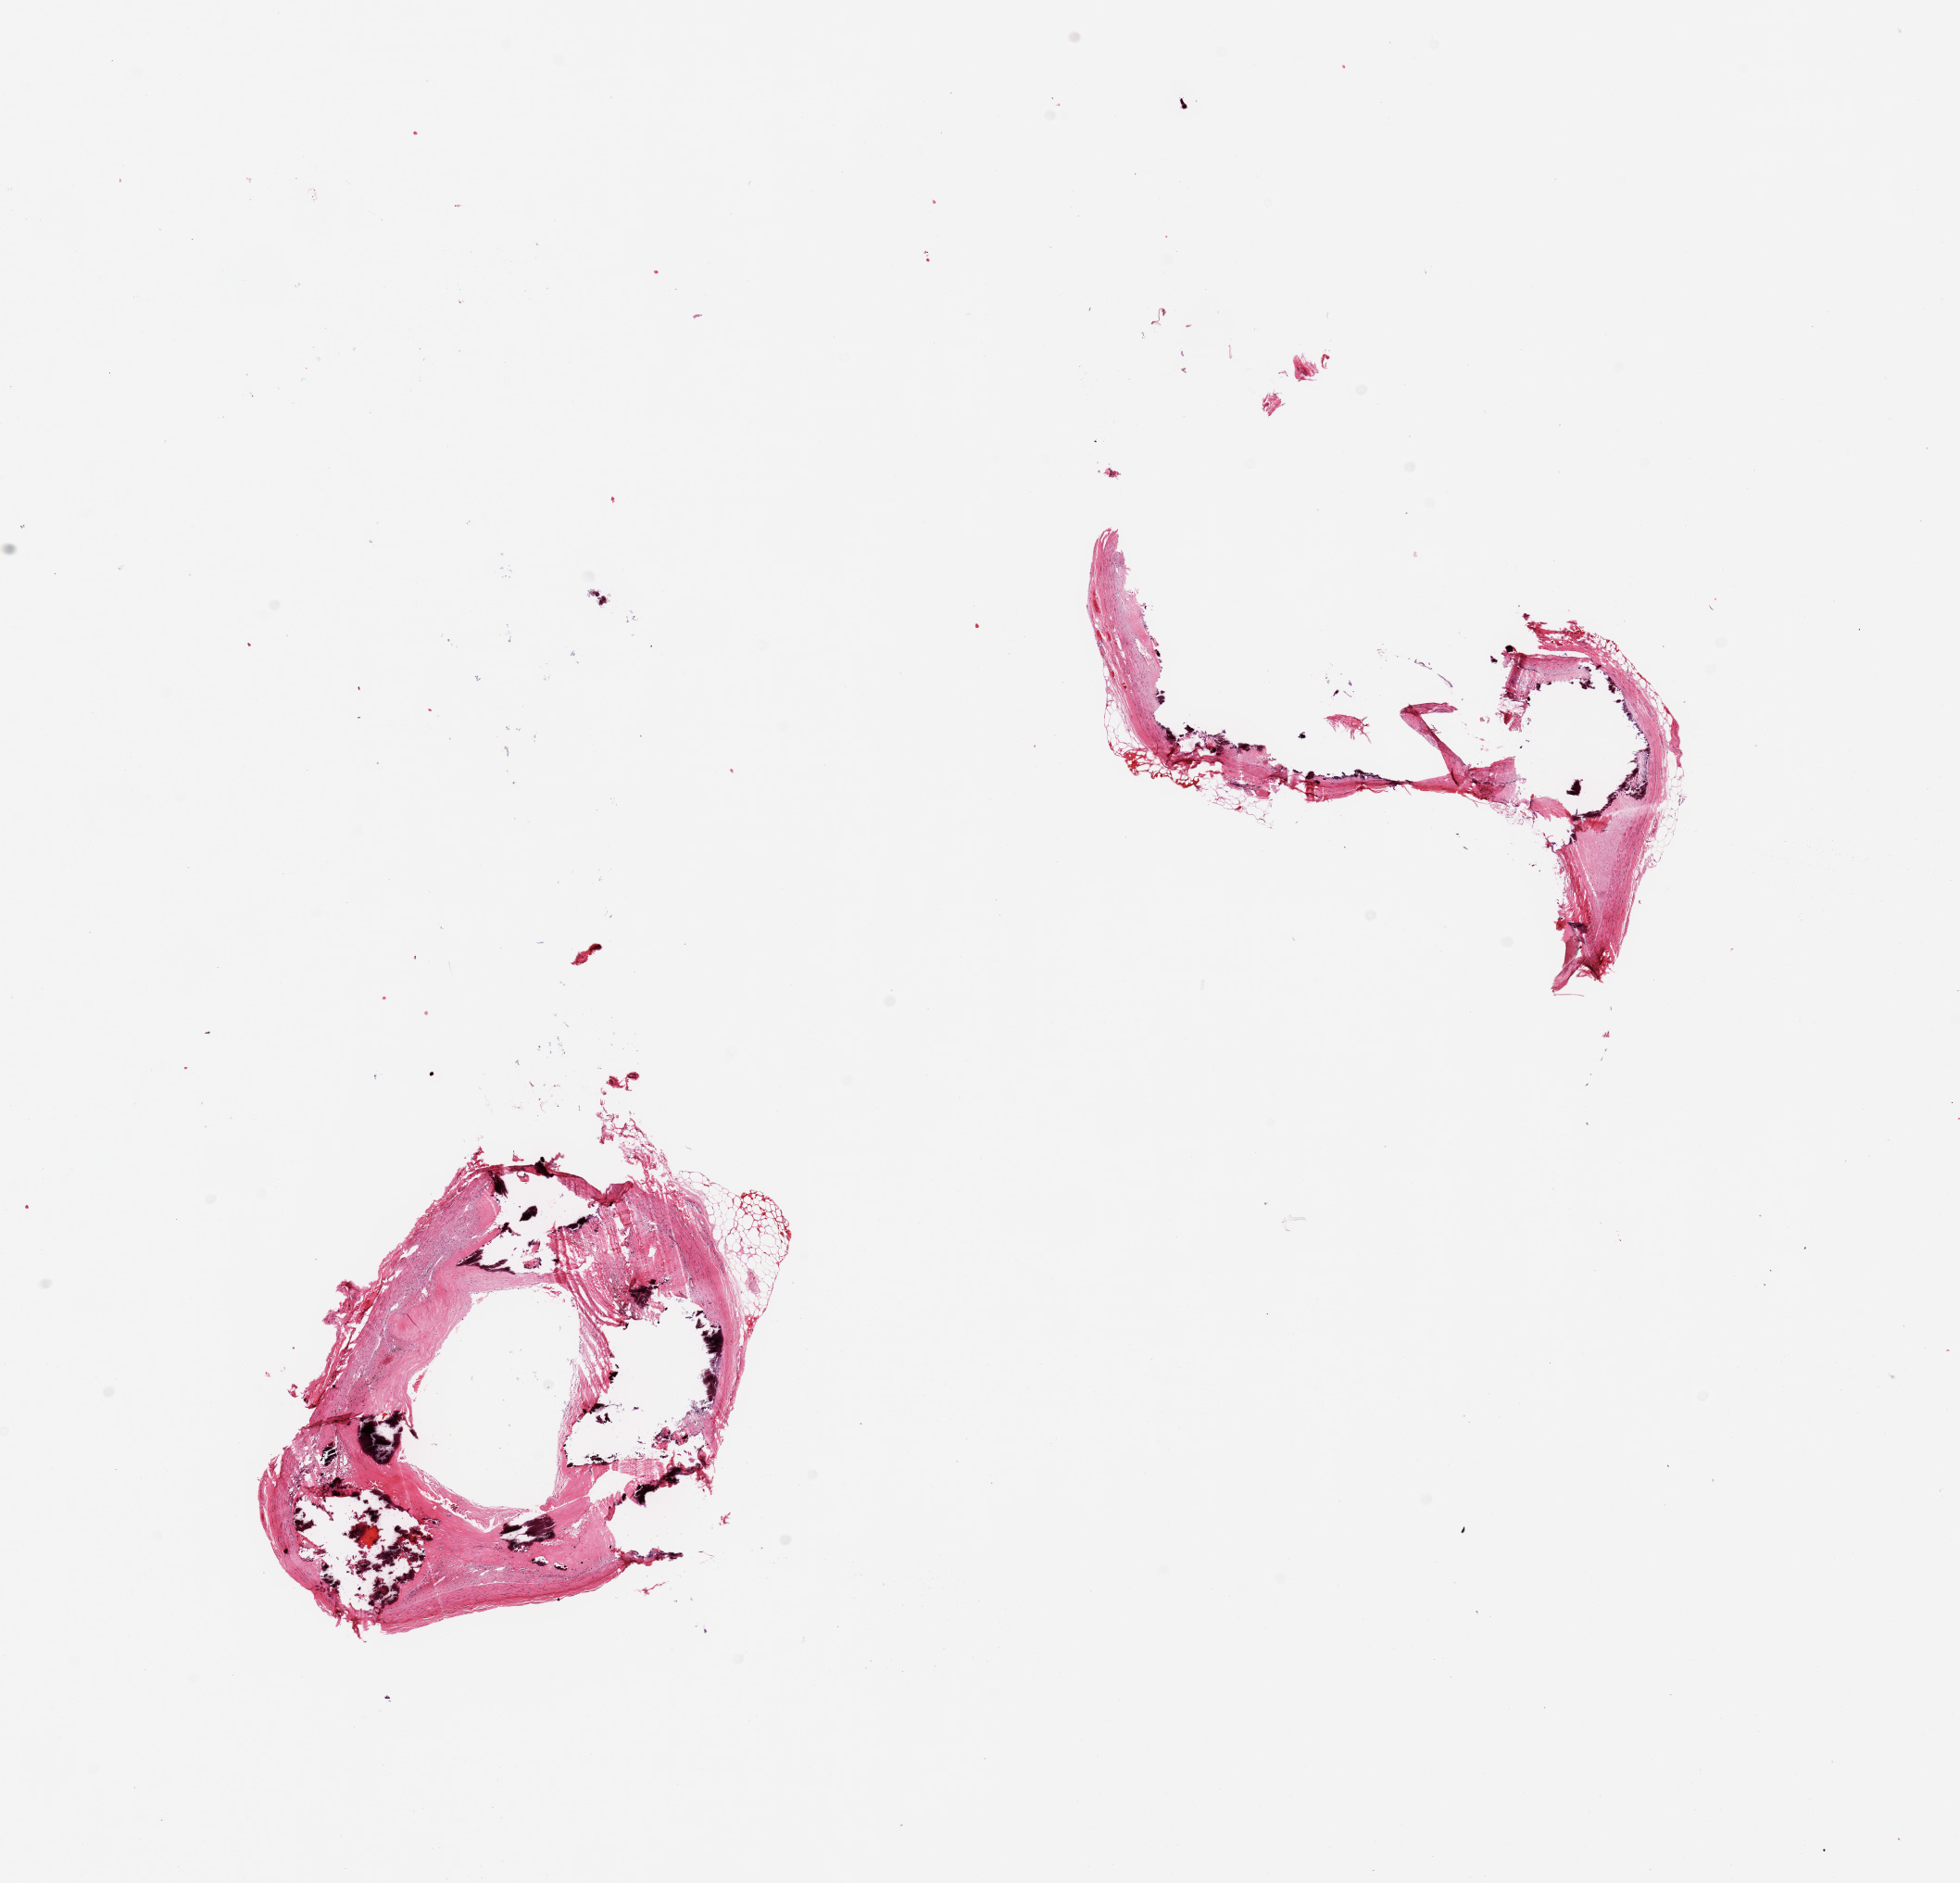
Whole-slide image, H&E stain — whole scanned area (about 16.7 x 16.1 mm, acquisition: 20x scan) shown as a low-resolution overview. PAXgene-fixed, paraffin-embedded tissue. Sampled site (target tissue): coronary artery. Tissue donor sample. Female donor.
Reviewer comment on this tissue sample: 2 pieces; 90% fibrocalcific tissue.